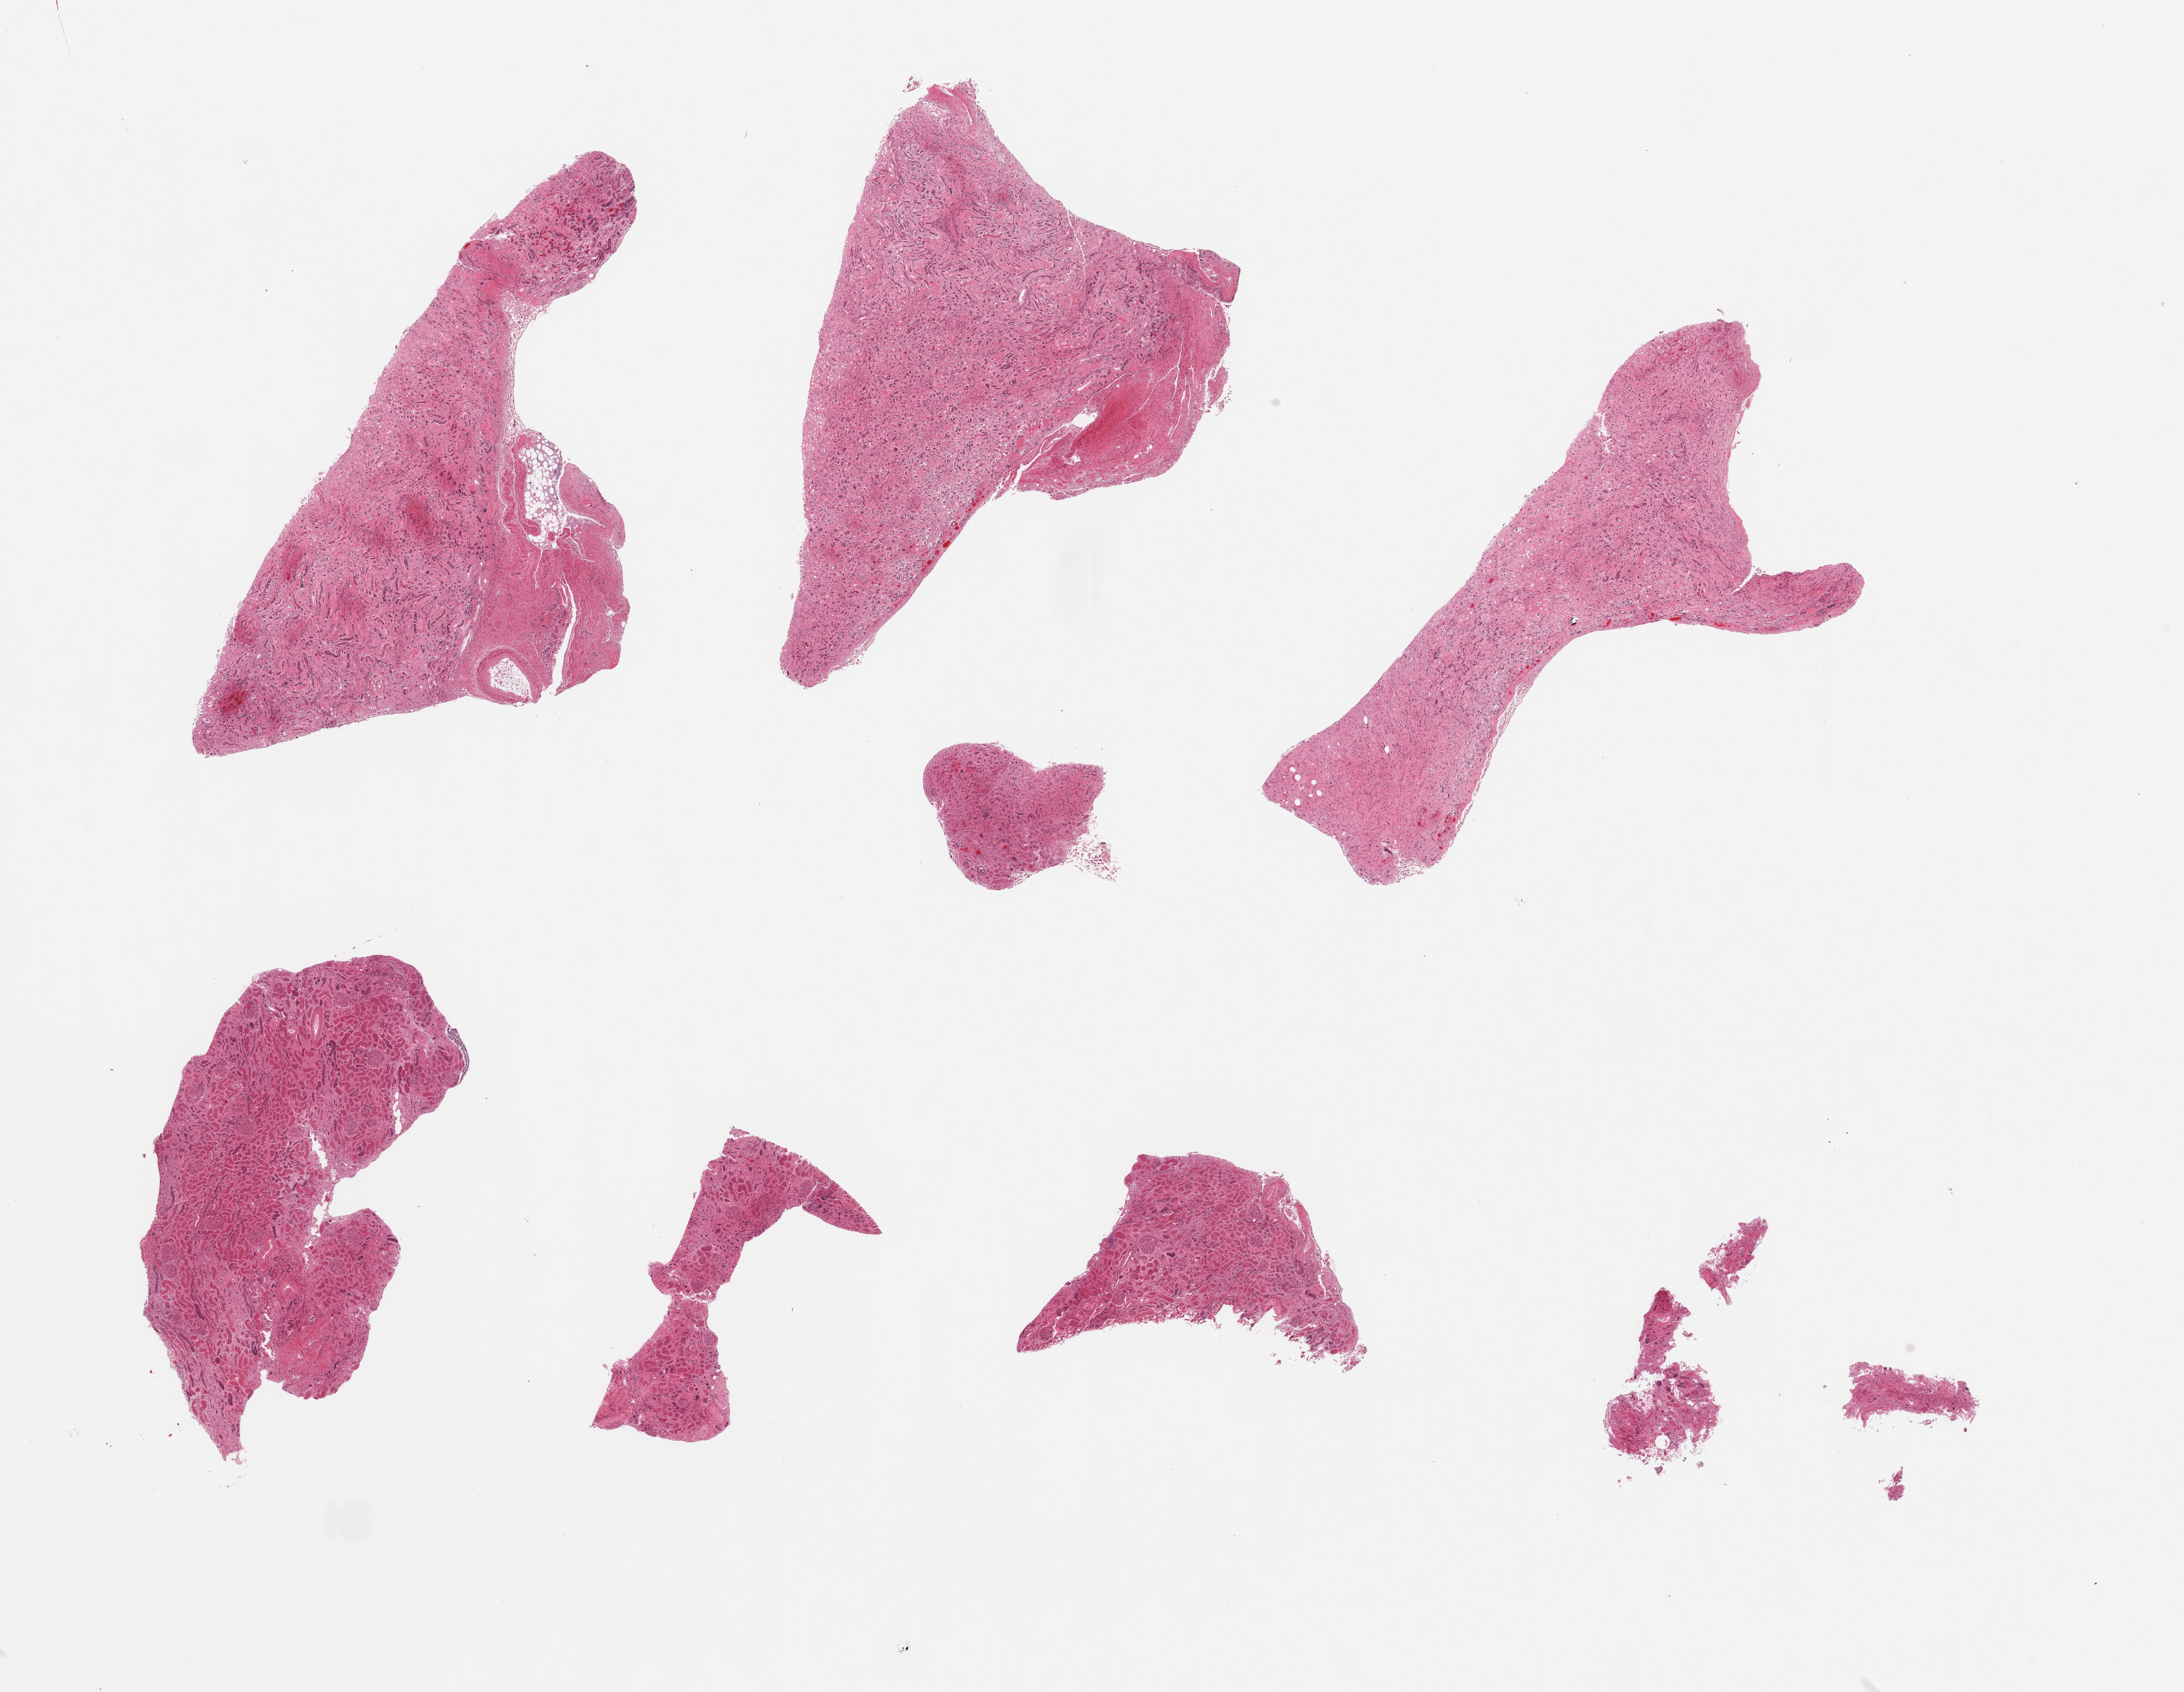
Whole-slide image, hematoxylin and eosin (H&E) stain — shown as a low-resolution overview of the whole scanned area (about 25.6 x 19.8 mm), PAXgene-fixed, paraffin-embedded tissue, section of renal cortex (target tissue), tissue donor sample. Donor sex: male.
Review note (as recorded): 8 pieces; fragmented renal parenchyma, <50% is renal cortex (target).